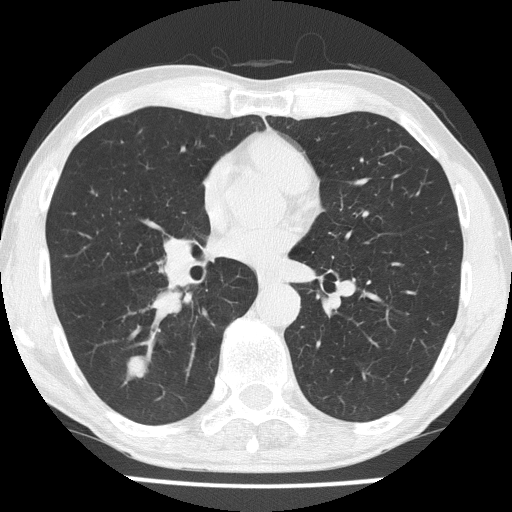
Low-dose screening chest CT, axial slice. Third screening round (two years after baseline). Lung window (W 1500 / L -600 HU). 2 mm slice thickness. Slice 103 of 186 in the series. Male, age 59 years at enrolment.
• Expert-annotated lung lesion, bounding box [x1, y1, x2, y2] px = [113, 346, 158, 391].
• The exam's reader record, not a measurement of the box and not confirmed to be the same lesion: non-calcified nodule or mass ≥4 mm, right lower lobe, 20 × 16 mm, smooth margins, soft tissue attenuation, pre-existing on the prior screen: no.
• Lung cancer was diagnosed 25 days after this screen: small cell carcinoma, NOS, right lower lobe, stage IIA (AJCC 6th edition), 20 mm at pathology.